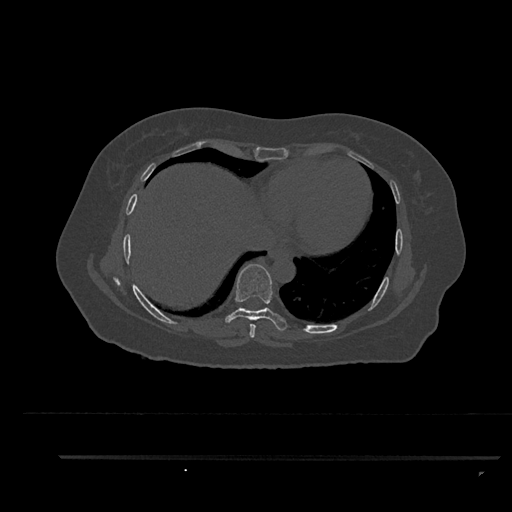
CT including the spine, one axial slice. Position 464 of 797 along the scan axis. Reconstruction kernel Br40s/3. Bone window (W 1800 / L 400 HU). 0.5 mm slice thickness. 512 × 512 image matrix. Patient: female, 44 years. From the clinical record (not read from this slice): primary cancer: renal.
Structures marked on this image (semi-automatic segmentation, software-assisted and operator-edited):
- T7 vertebra: box from (x=249, y=324) to (x=256, y=338) px
- T8 vertebra: (x=225, y=264)–(x=287, y=331)